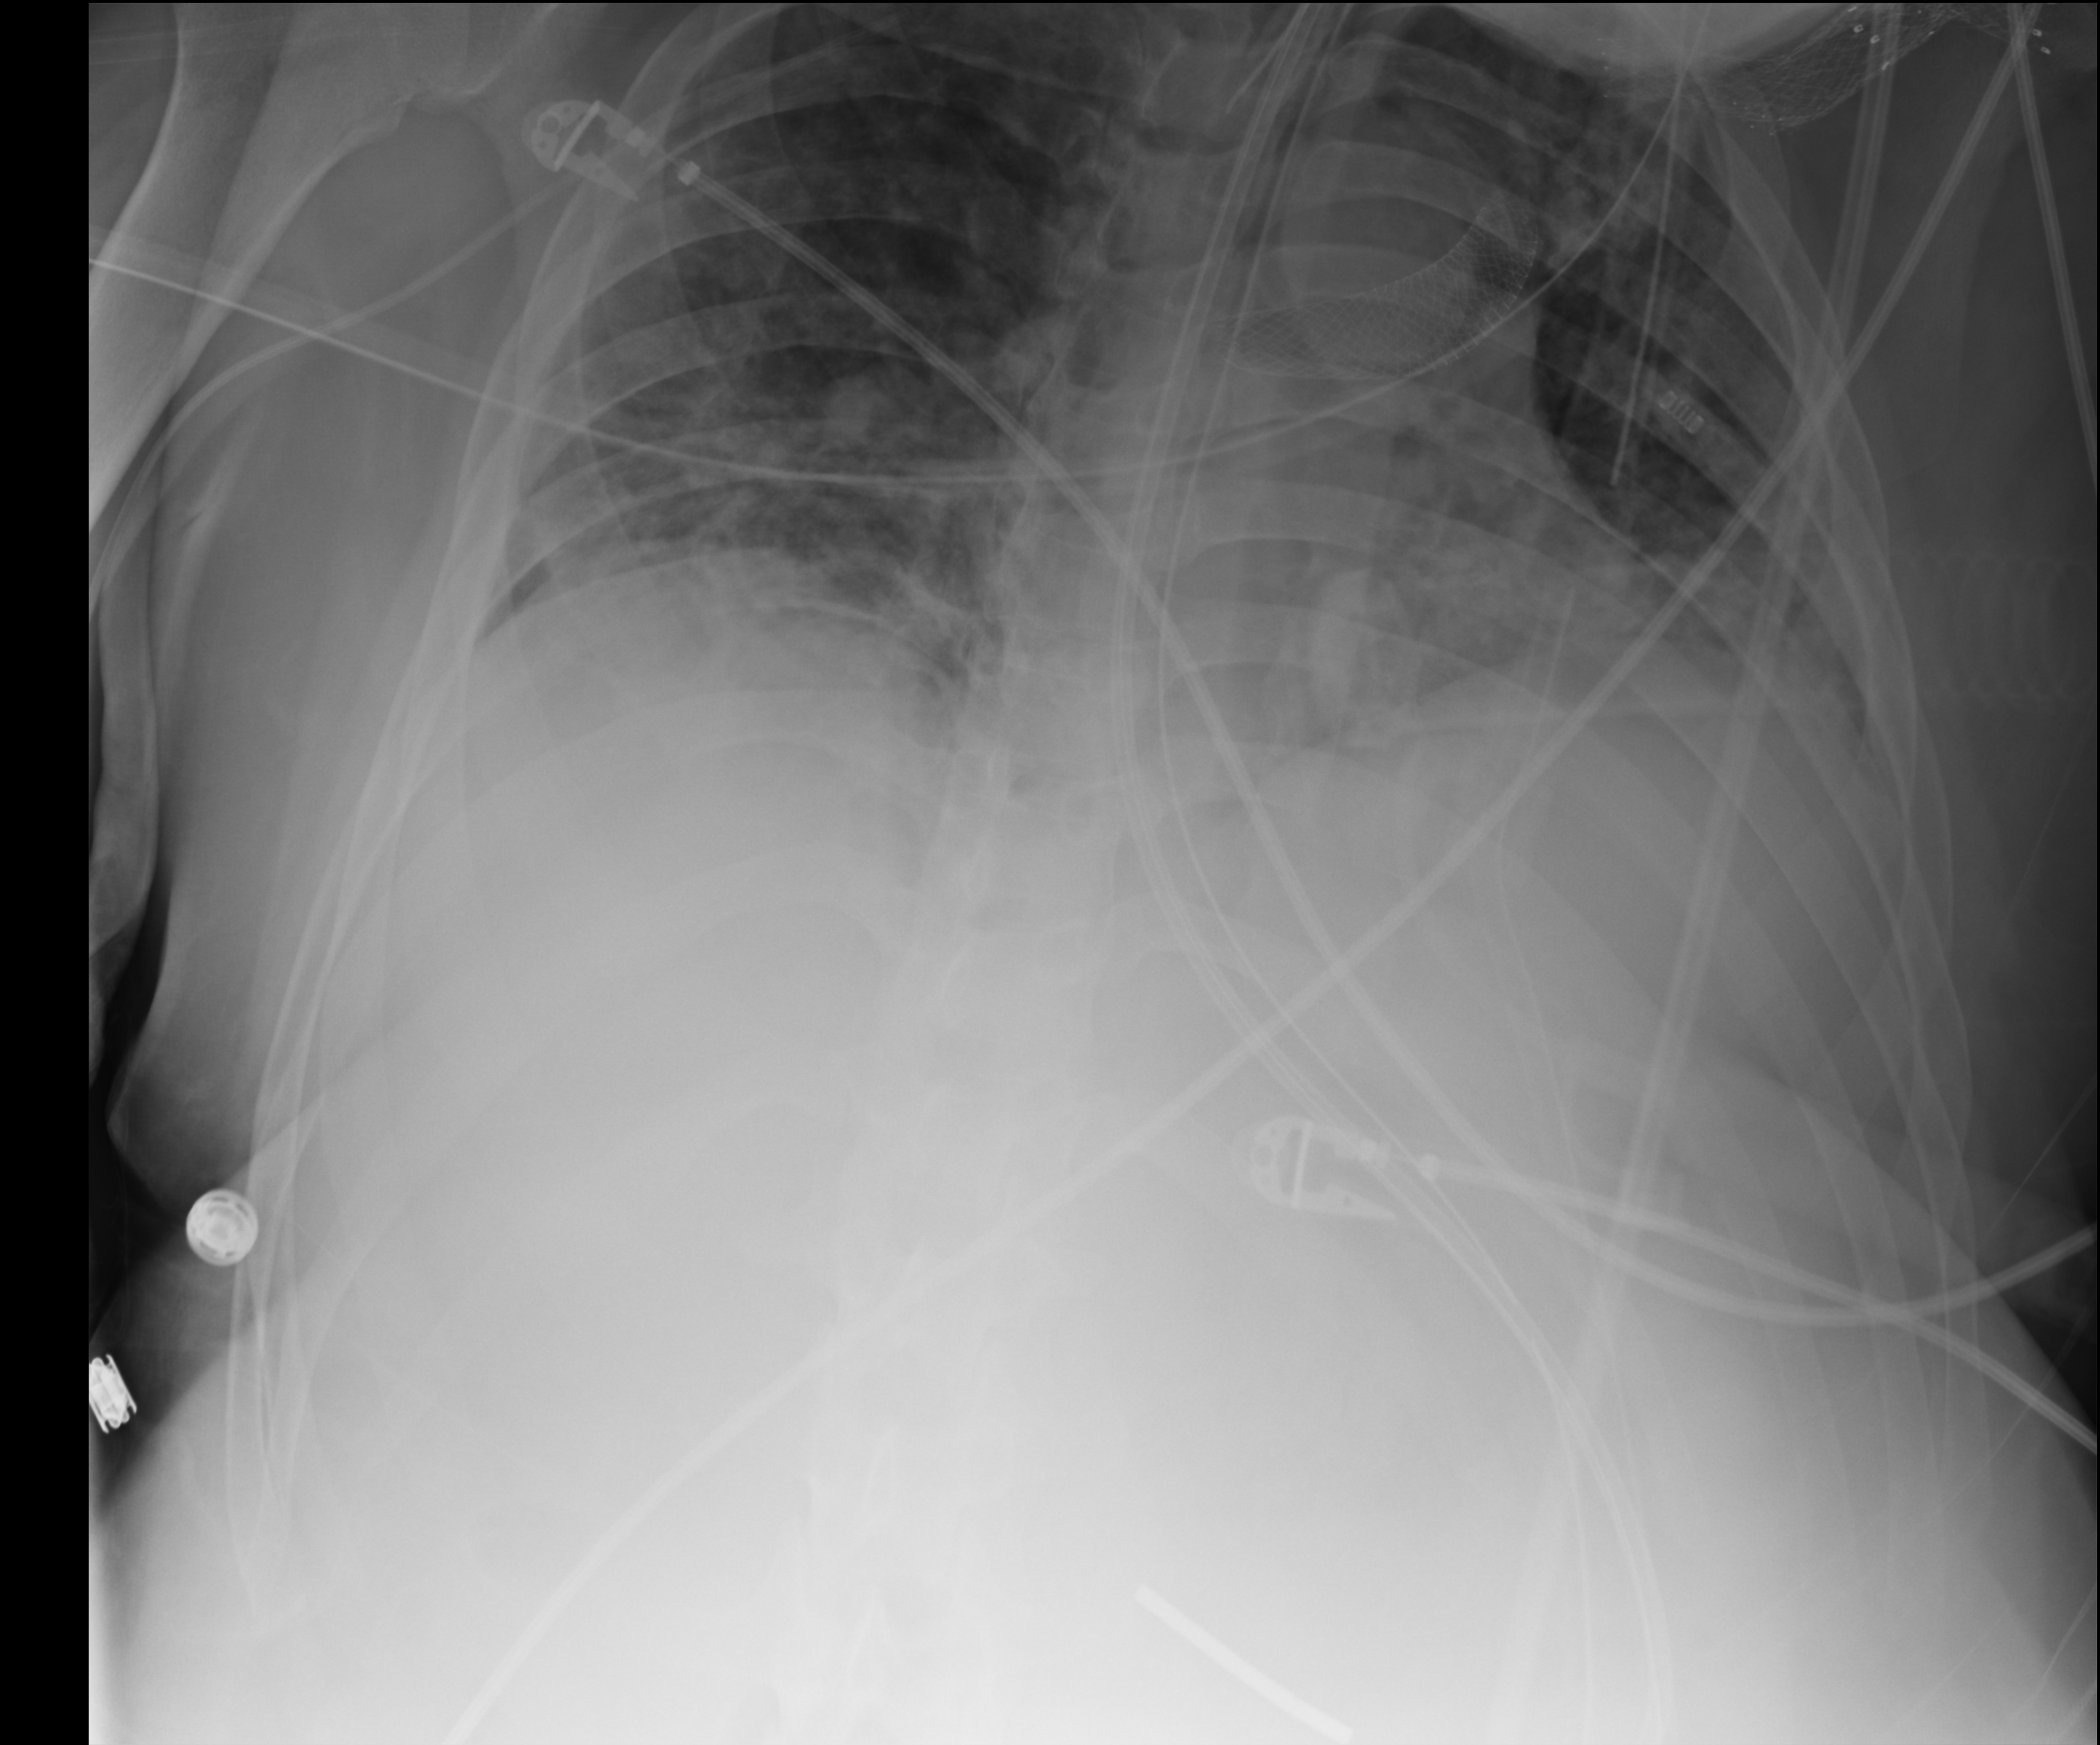
Portable chest radiograph. Male patient hospitalised with COVID-19, age 18–59 years.
Admission-level facts for this patient (not findings on this image; timing relative to this image not recorded):
- admitted to intensive care during this hospital stay: yes
- length of hospital stay: 41 days